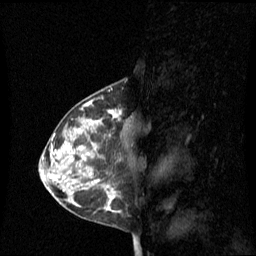
Breast MRI (dynamic contrast-enhanced), one sagittal slice. Slice 36 of 60 in the series (ordered by position). Dynamic contrast-enhanced series, image 2 of 3 at this slice position (ordered by acquisition). 1.5 T. TE 4.2 ms, TR 8.4 ms. 2.1 mm slice thickness. 256 × 256 image matrix, field of view 240 × 240 mm. Female patient, age 42 years. Case-level facts recorded for this patient, not image findings: setting: breast cancer imaged before/during neoadjuvant chemotherapy; receptor status: HR-positive, HER2-negative.
Structures marked on this image (semi-automatic segmentation, software-assisted and operator-edited):
- analysis volume of interest (the breast-tissue region the enhancement analysis was run in; not a lesion): box from (x=68, y=110) to (x=125, y=201) px
- tumour enhancement mask (voxels above the 70 % enhancement threshold inside the analysis volume of interest): (x=88, y=110)–(x=121, y=201)